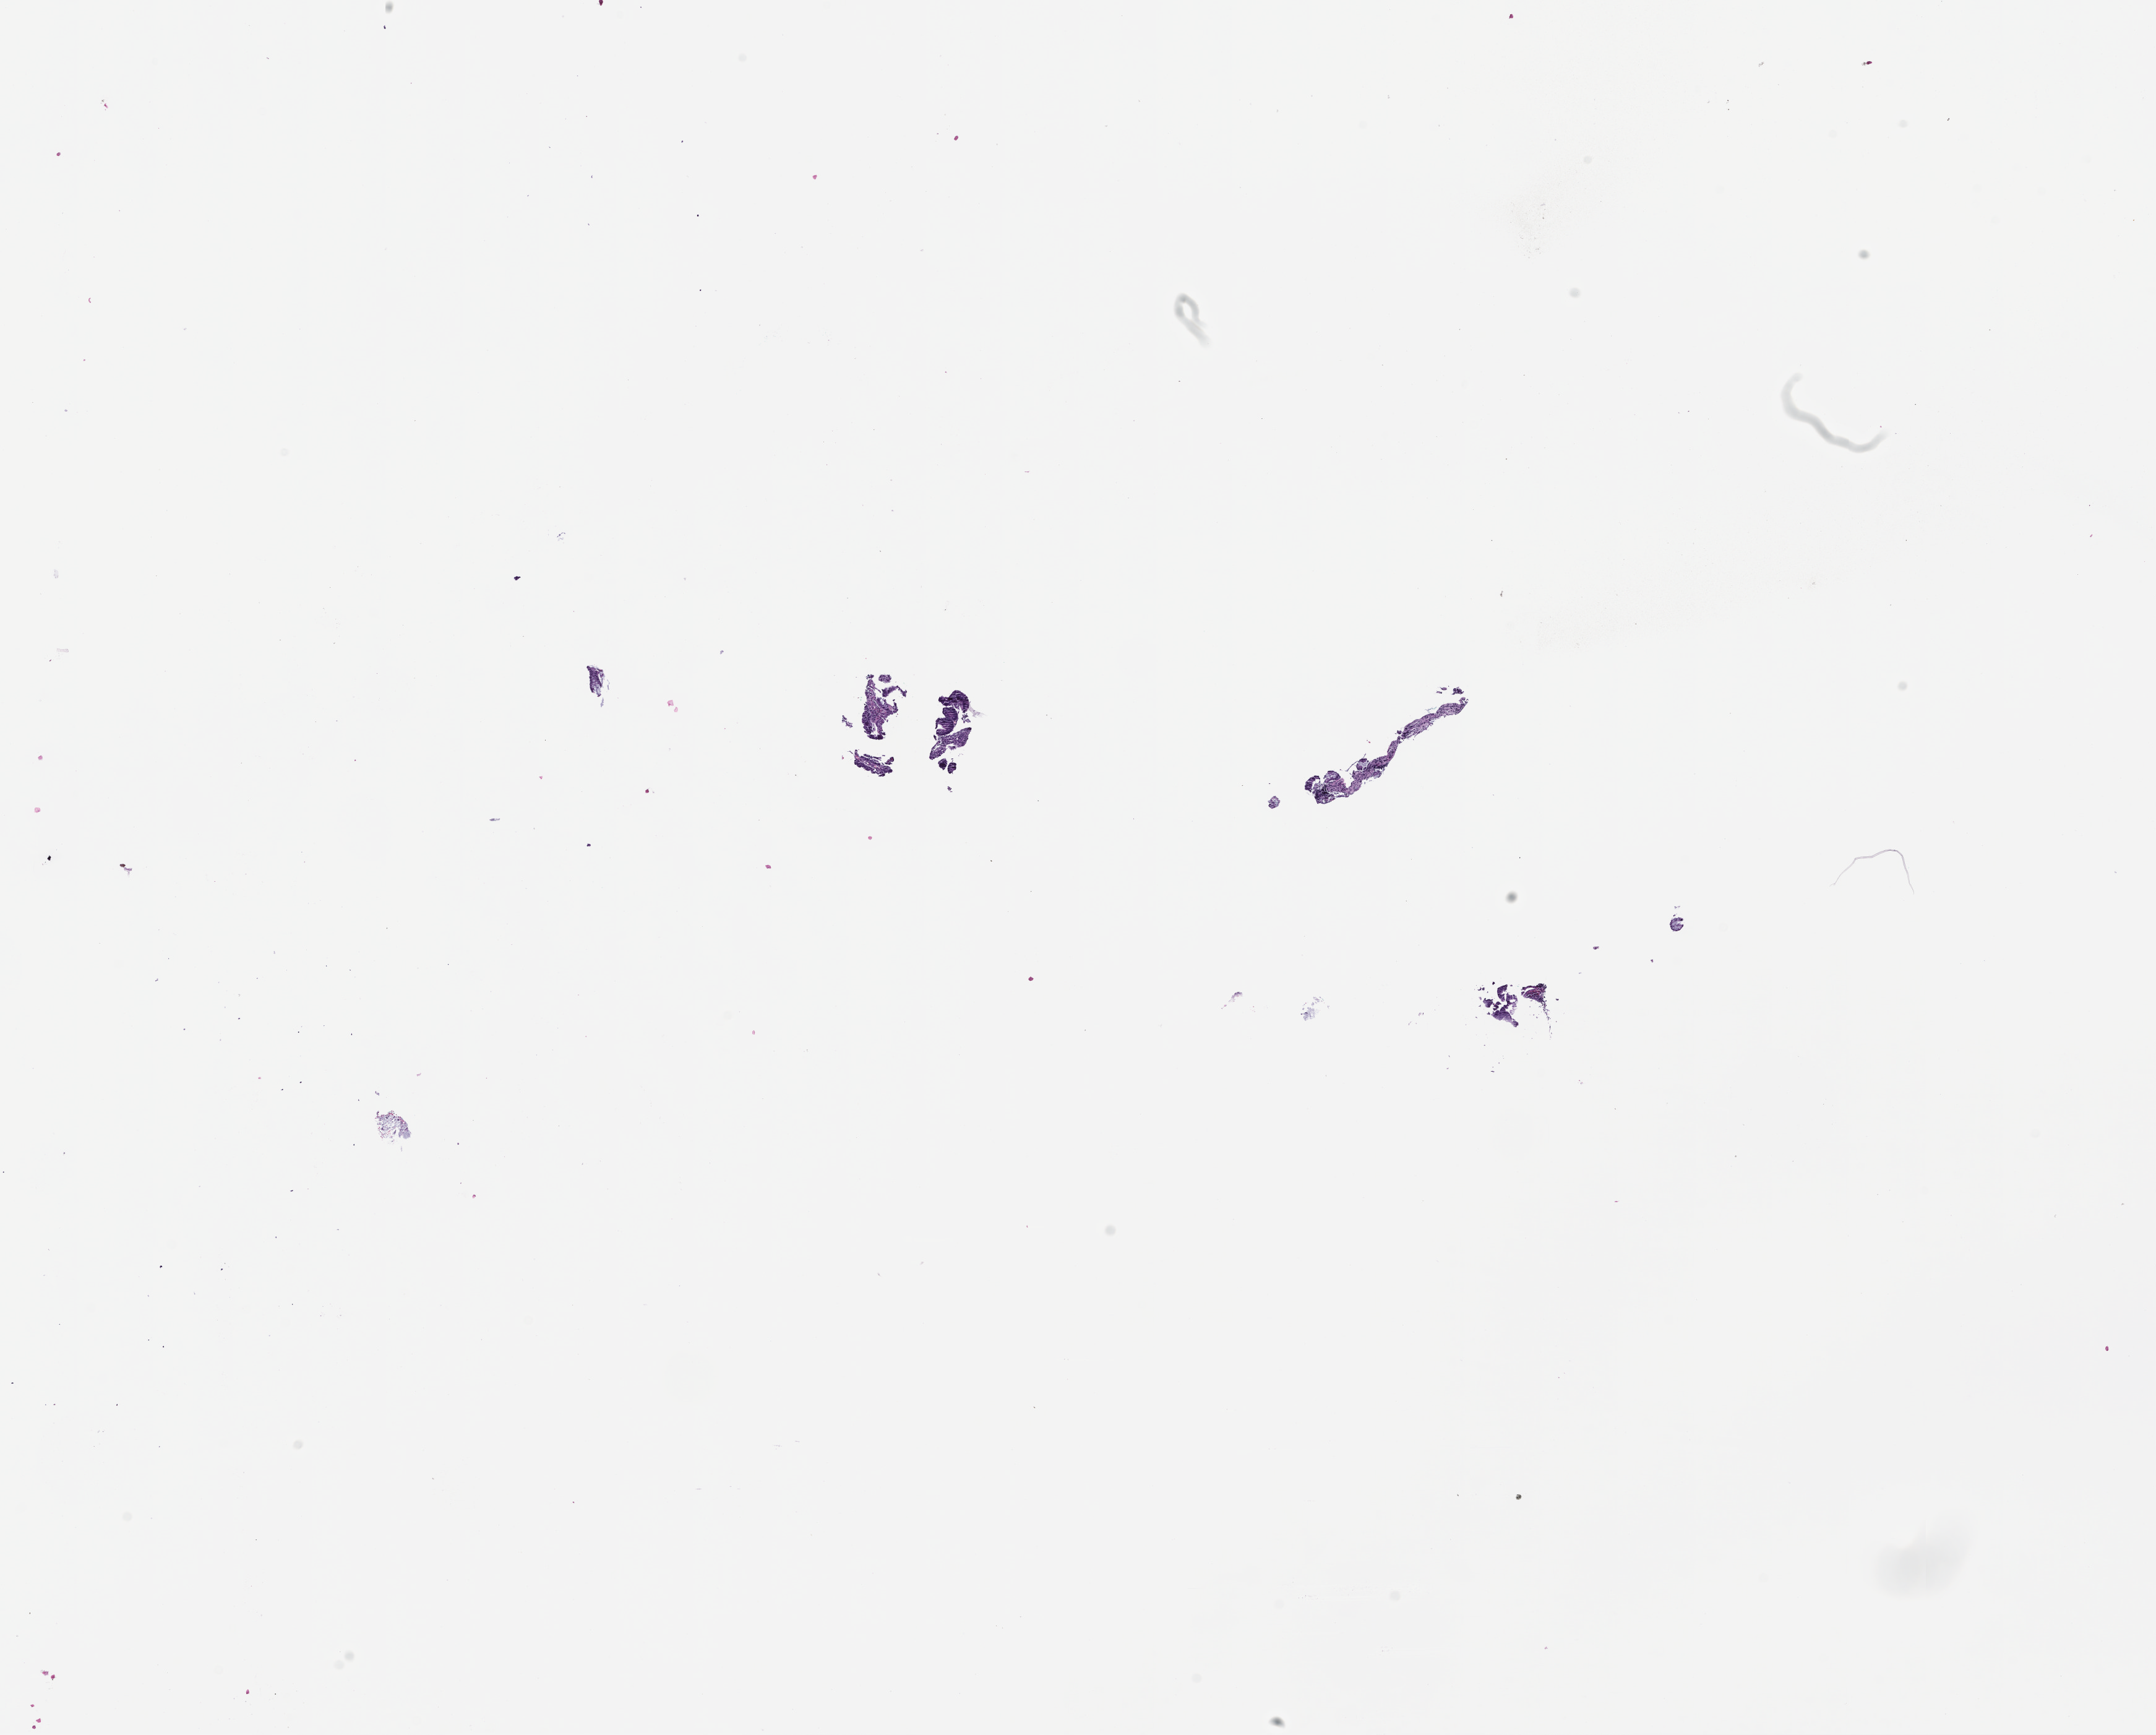
Whole-slide image, hematoxylin and eosin (H&E) stain — whole scanned area (about 14.1 x 11.3 mm) shown as a low-resolution overview. Formalin-fixed, paraffin-embedded (FFPE) tissue. Tissue site: colon. Male patient.
• this section: primary tumour tissue
• diagnosis: Colorectal Carcinoma